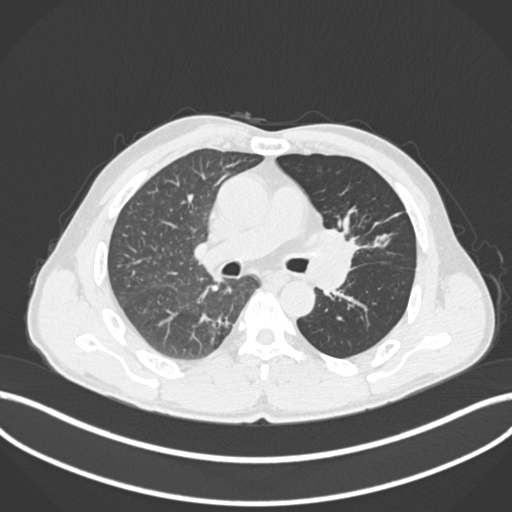
Chest CT, one axial slice. Slice 110 of 255 in the series (ordered by position). 120 kVp. Lung window (W 1500 / L -600 HU). 1 mm slice thickness. 512 × 512 image matrix, field of view 400 × 400 mm. Patient: male, 57 years. From the clinical record (not read from this slice): clinical TNM (as recorded): T2b N0 M0.
Annotated regions visible in this slice (bounding box drawn by a radiologist):
- lung tumour (recorded histology: squamous cell carcinoma): bounding box (x1, y1, x2, y2) in pixels: (312, 224, 365, 263)